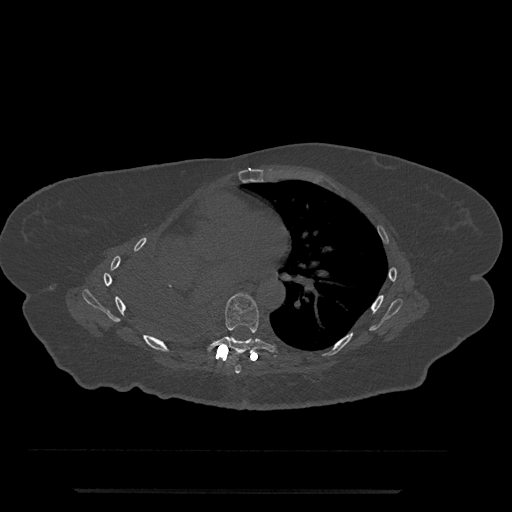
CT including the spine, one axial slice. Slice 445 of 797 in the series (ordered by position). 120 kVp. Bone window (W 1800 / L 400 HU). 0.5 mm slice thickness. 512 × 512 image matrix, field of view 440 × 440 mm. Patient: female, 51 years. Case-level facts recorded for this patient, not image findings: primary cancer: neuro.
Outlined on this slice (semi-automatic segmentation, software-assisted and operator-edited):
- T6 vertebra: bounding box <235,365,241,374> (left, top, right, bottom; pixels)
- T7 vertebra: <206,293,279,356>